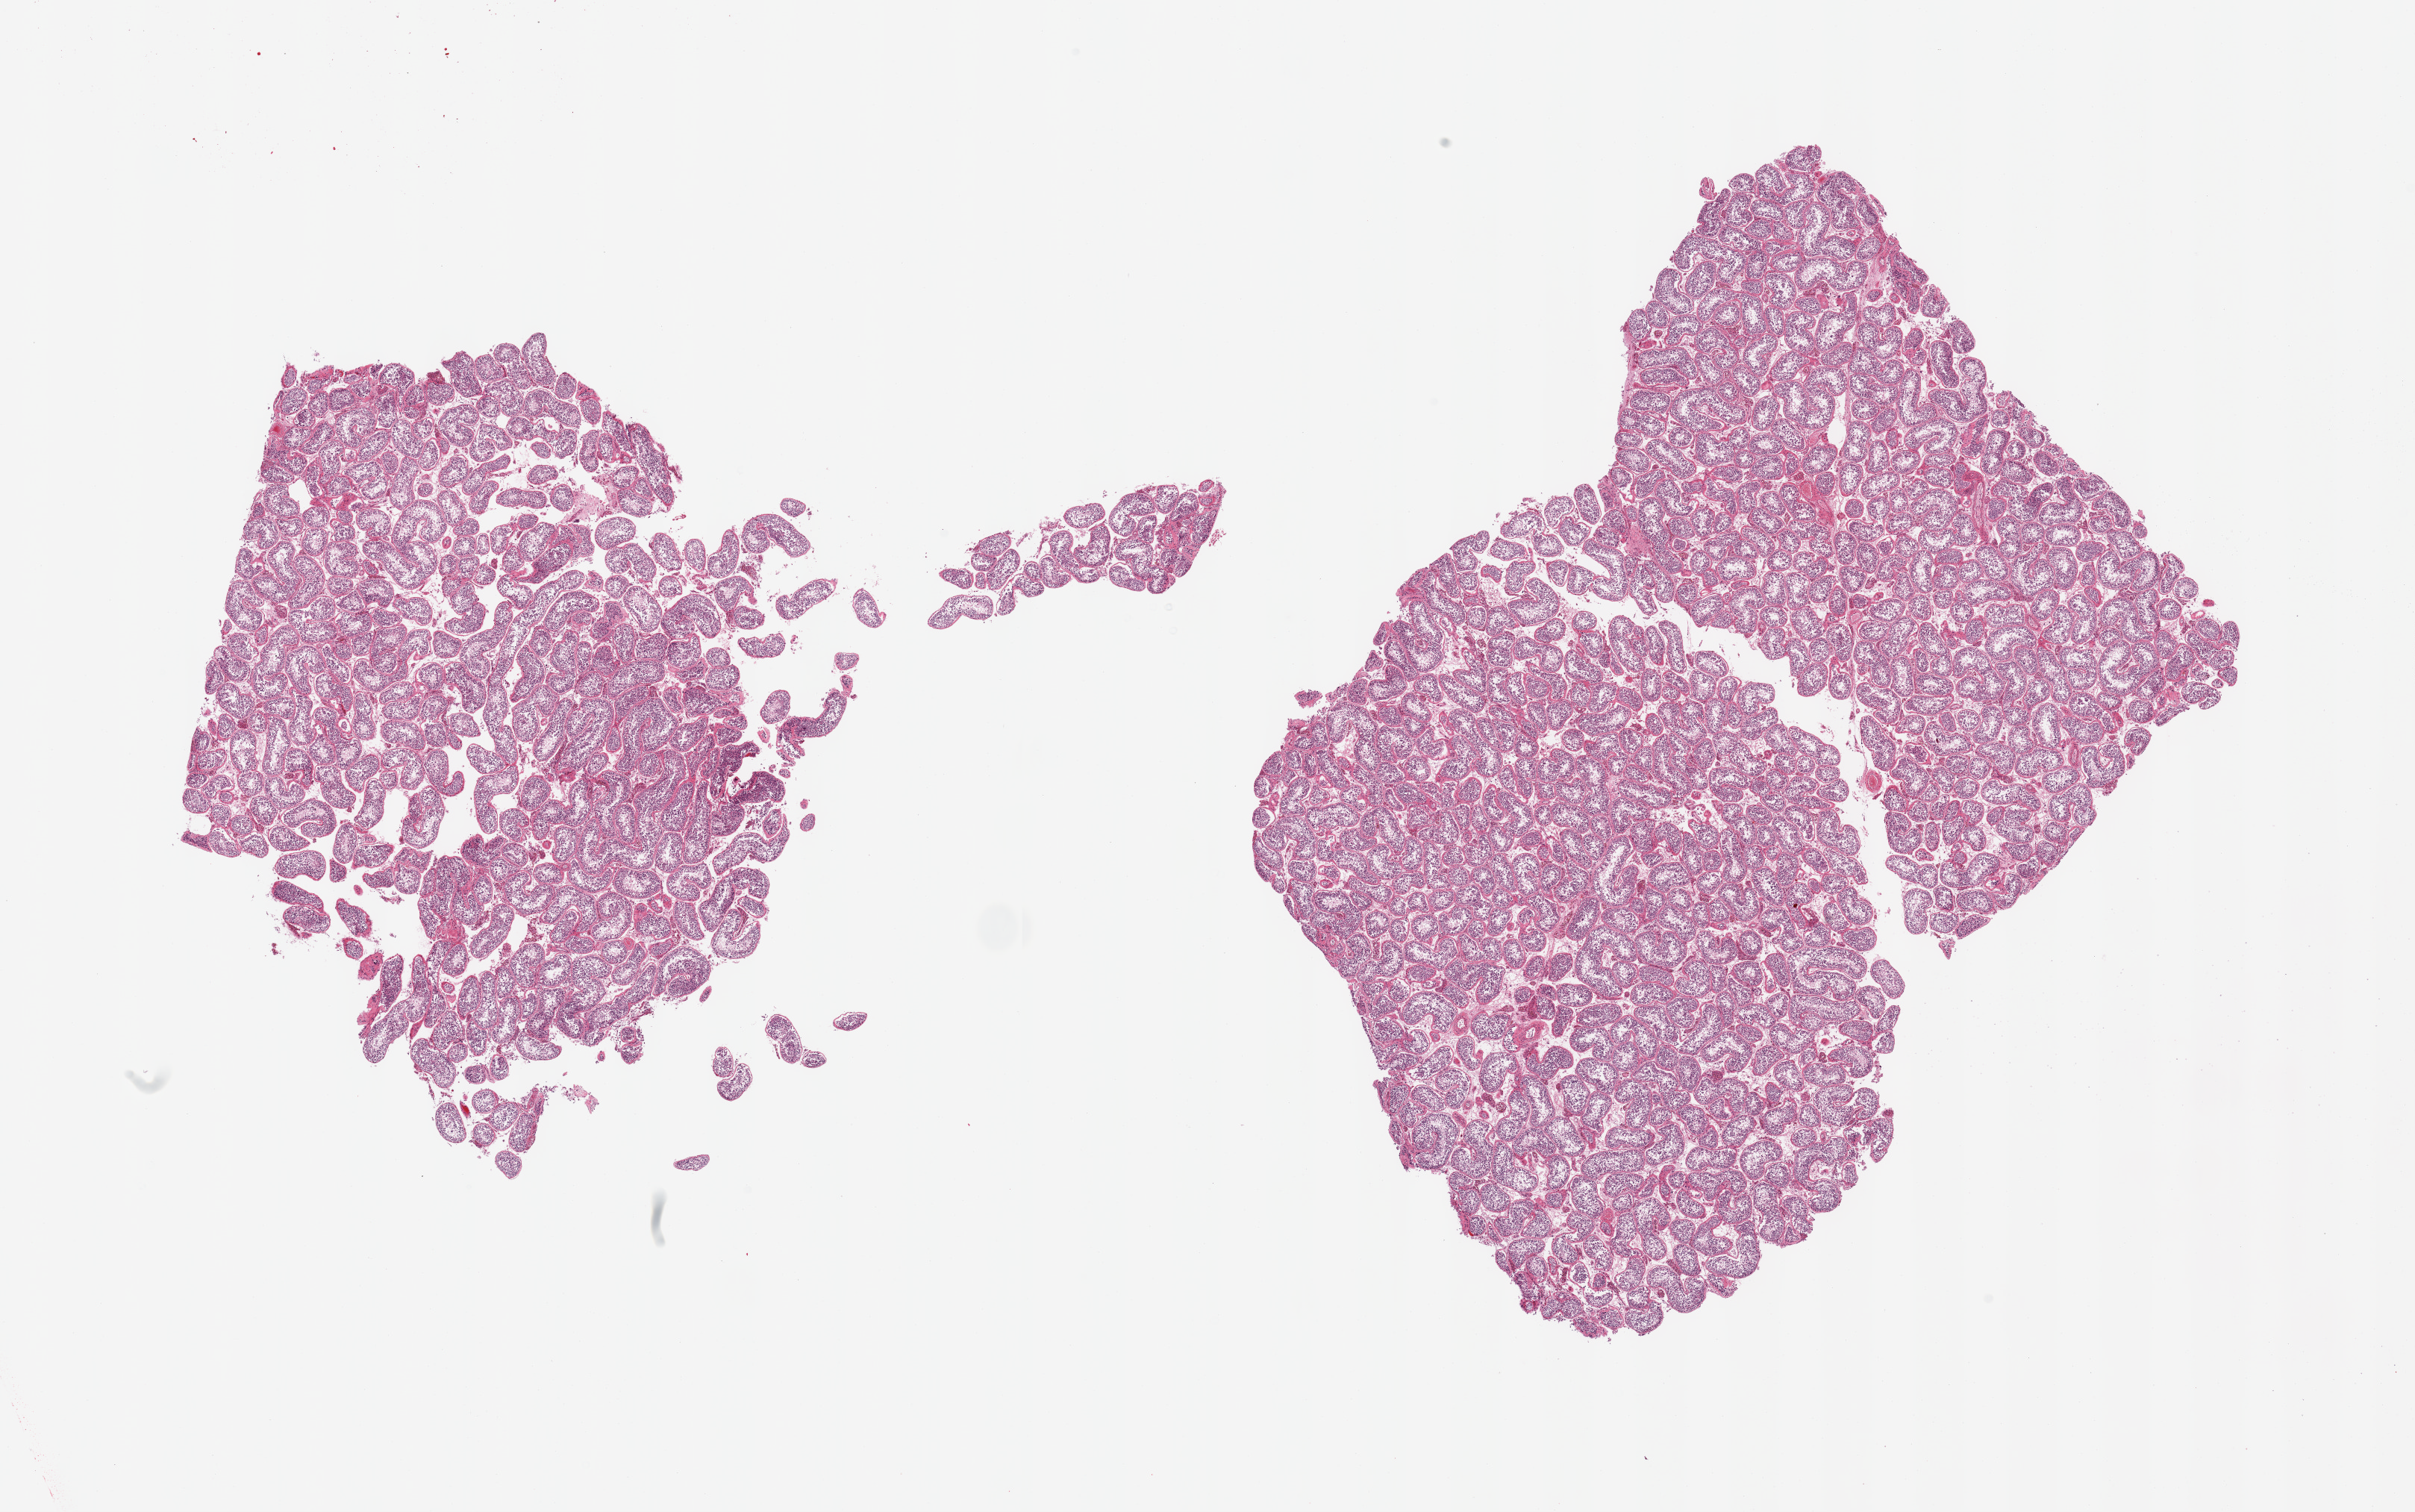
Whole-slide image, haematoxylin and eosin stain, a low-resolution overview of the entire scanned area, about 25.6 x 16.0 mm. PAXgene-fixed, paraffin-embedded tissue. Target tissue: testis. Tissue donor sample. Donor: male.
• review note (as recorded): 2 pieces; spermatogenesis is present